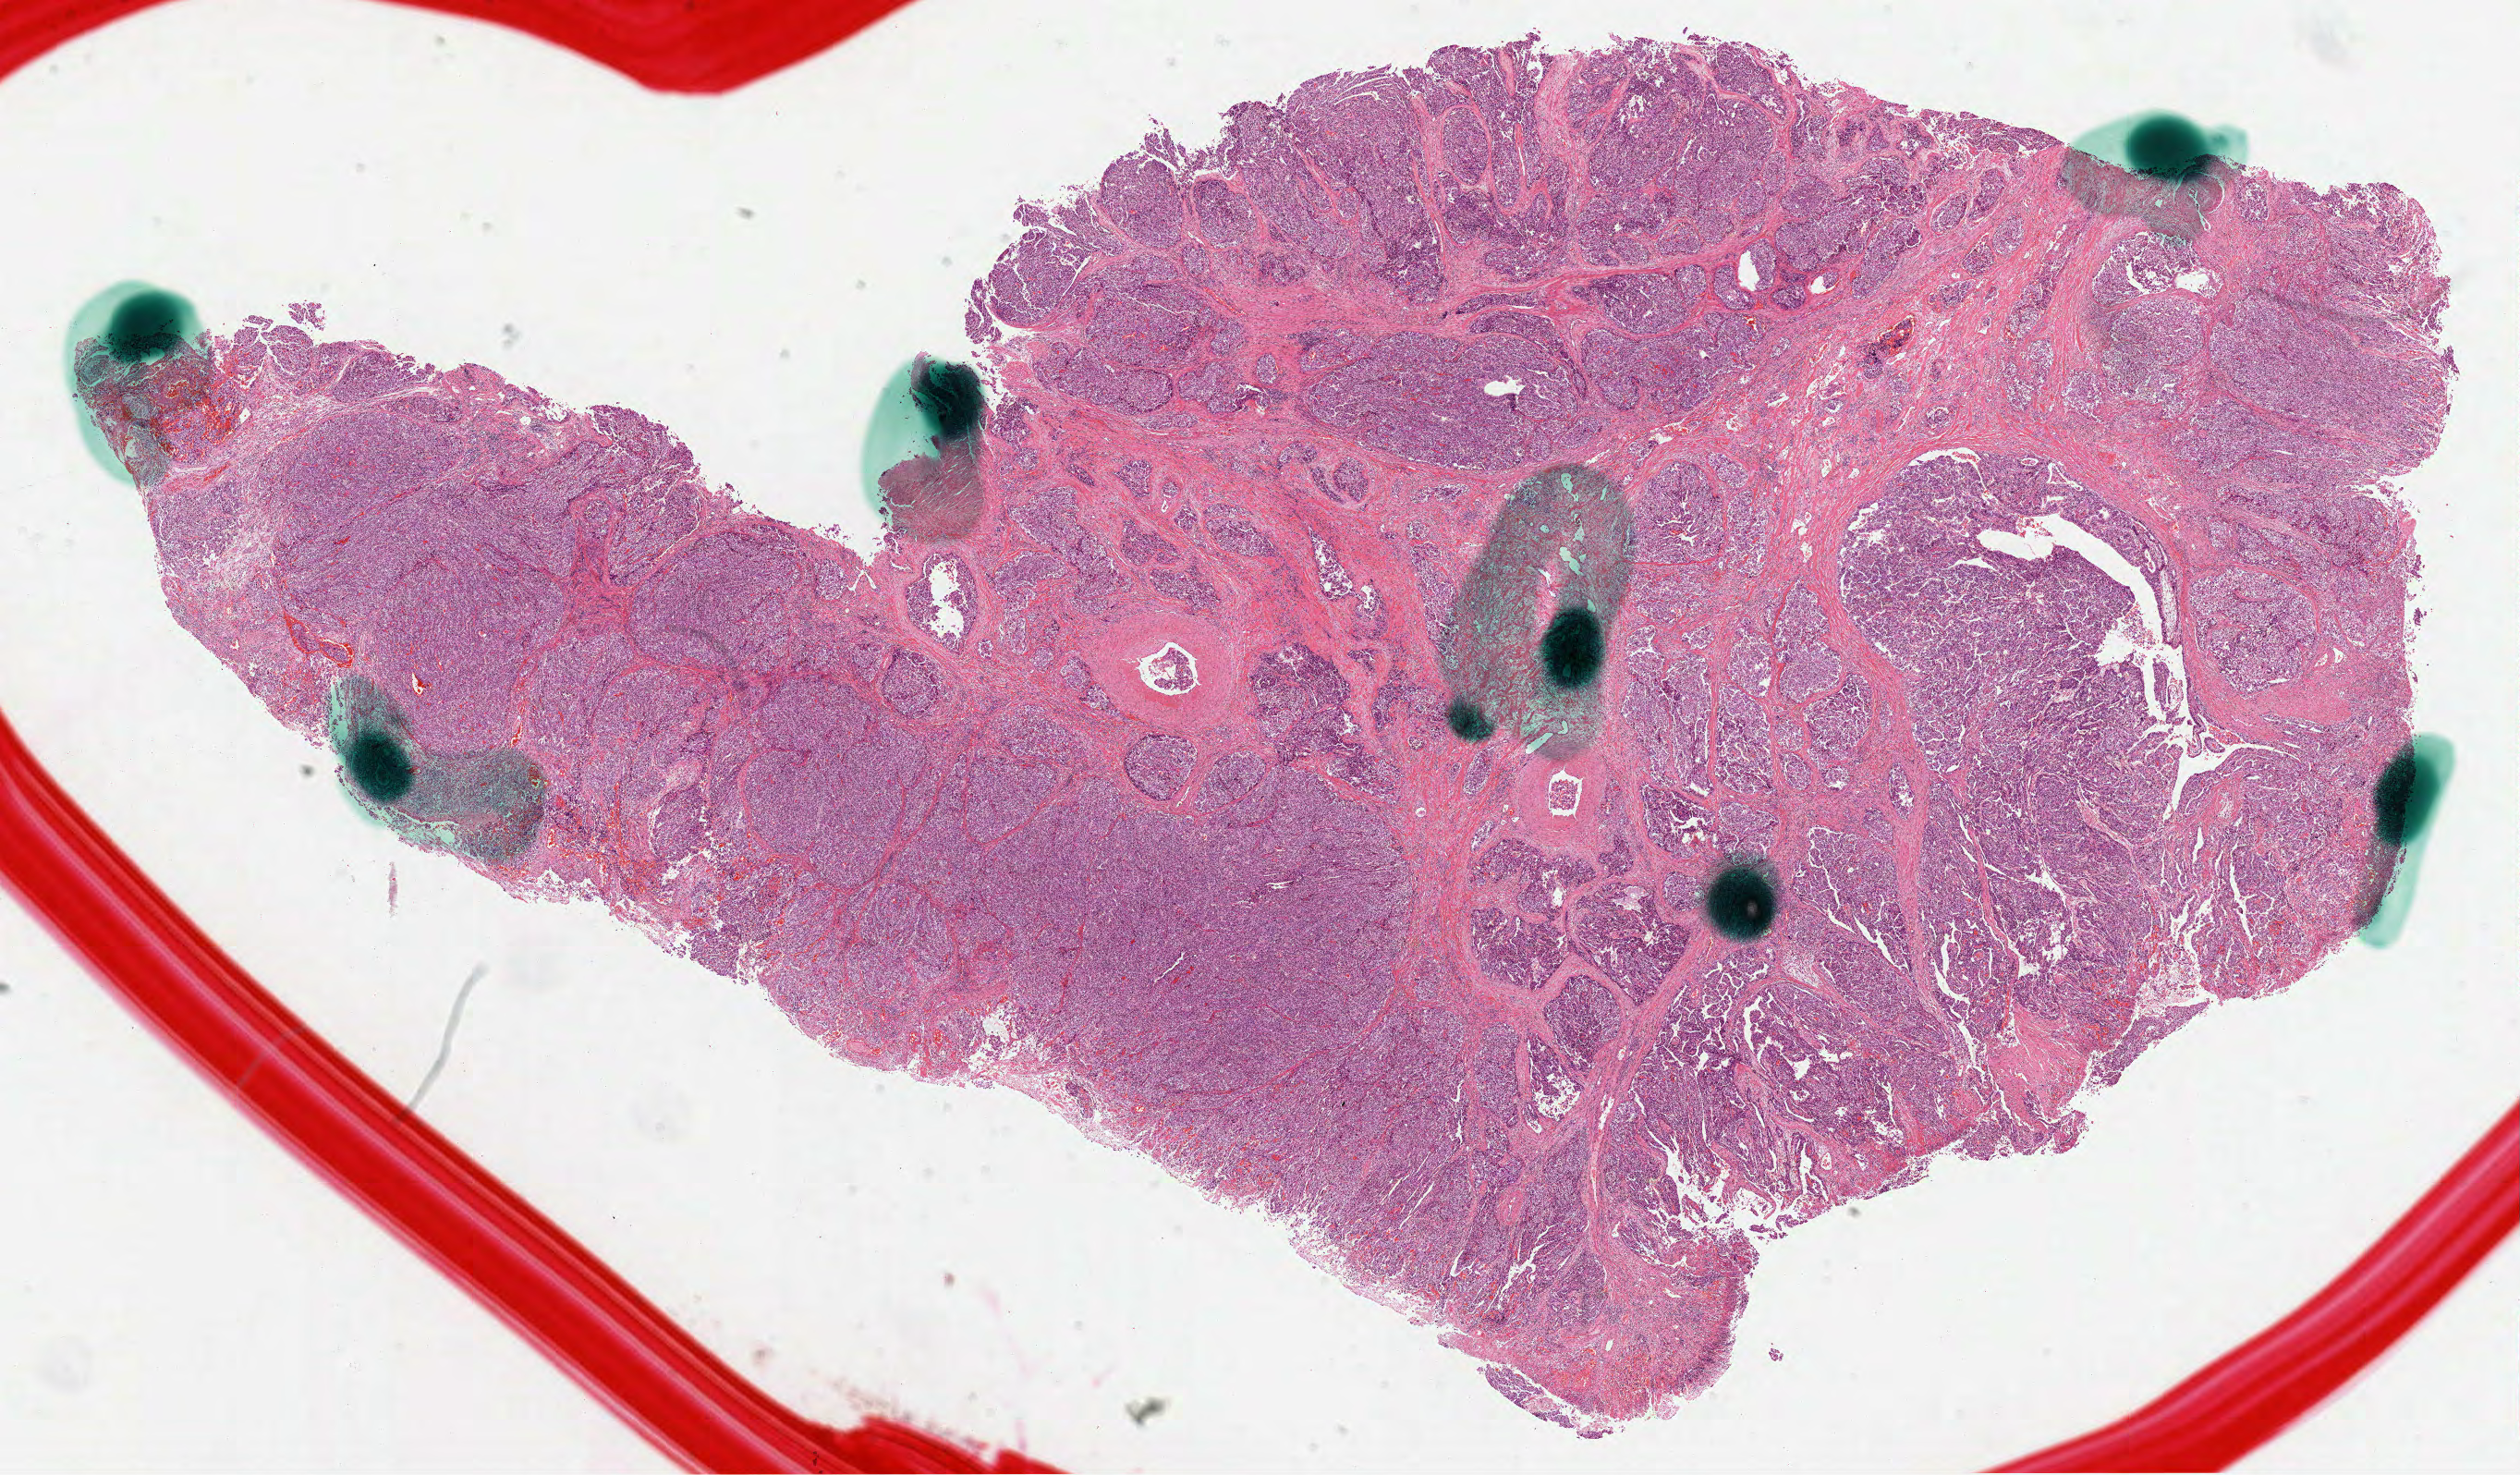
Whole-slide histology image, H&E-stained — shown as a low-resolution overview of the whole scanned area (about 22.0 x 12.9 mm, from a 40x scan), formalin-fixed paraffin-embedded (FFPE) diagnostic section, stomach, primary tumour sample. Female patient; age at initial diagnosis 60 years. Histologic grade: G3 (poorly differentiated).
- AJCC pathologic stage: IIB (7th edition)
- pathologic diagnosis: Adenocarcinoma, intestinal type (body of stomach)
- TNM: T4a N0 M0
- lymph nodes positive (case pathology): 0 of 5 examined